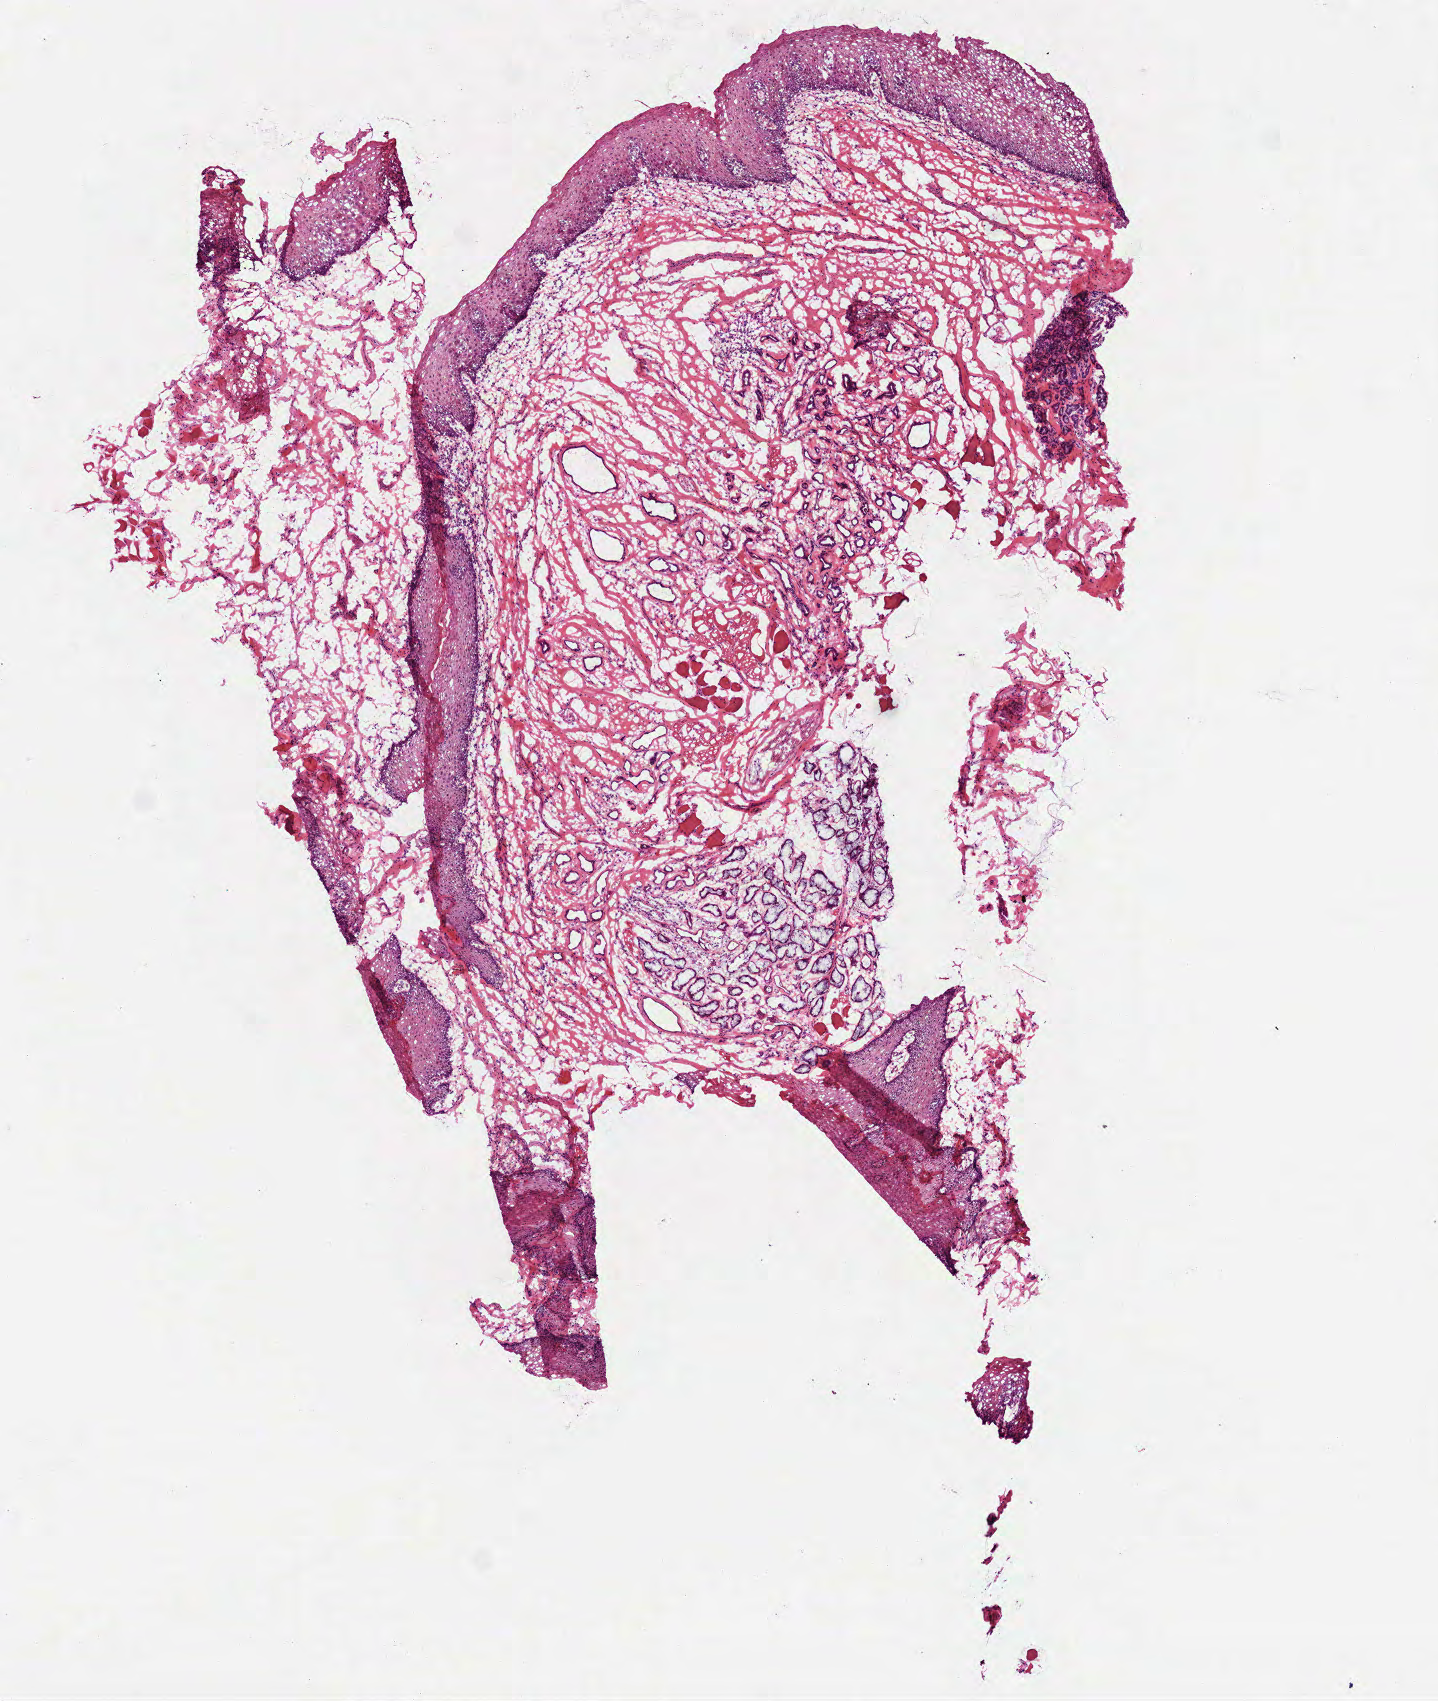
Whole-slide histology image, H&E-stained — low-resolution overview of the scanned area, about 5.8 x 6.9 mm (from a 40x scan). Frozen section from the top of the tissue portion. Sample: solid tissue normal (non-tumour tissue), head and neck. Patient: female, age at initial diagnosis 62 years.
* this section: solid tissue normal sample (biorepository sample class)
* patient diagnosis: Squamous cell carcinoma, NOS (overlapping lesion of lip, oral cavity and pharynx)